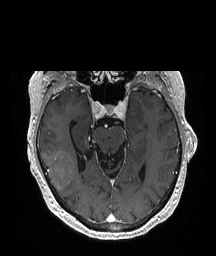
Brain MRI from a brain-tumour surgery series, one axial slice; position 130 of 208 along the scan axis; T1-weighted post-contrast; 1 mm slice thickness; 216 × 256 image matrix, field of view 216 × 256 mm. From the clinical record (not read from this slice): histopathology: Glioblastoma; WHO grade: 4; IDH mutation: no.
Structures marked on this image (expert manual segmentation):
- tumour: bounding box [x1, y1, x2, y2] px = [44, 151, 75, 192]